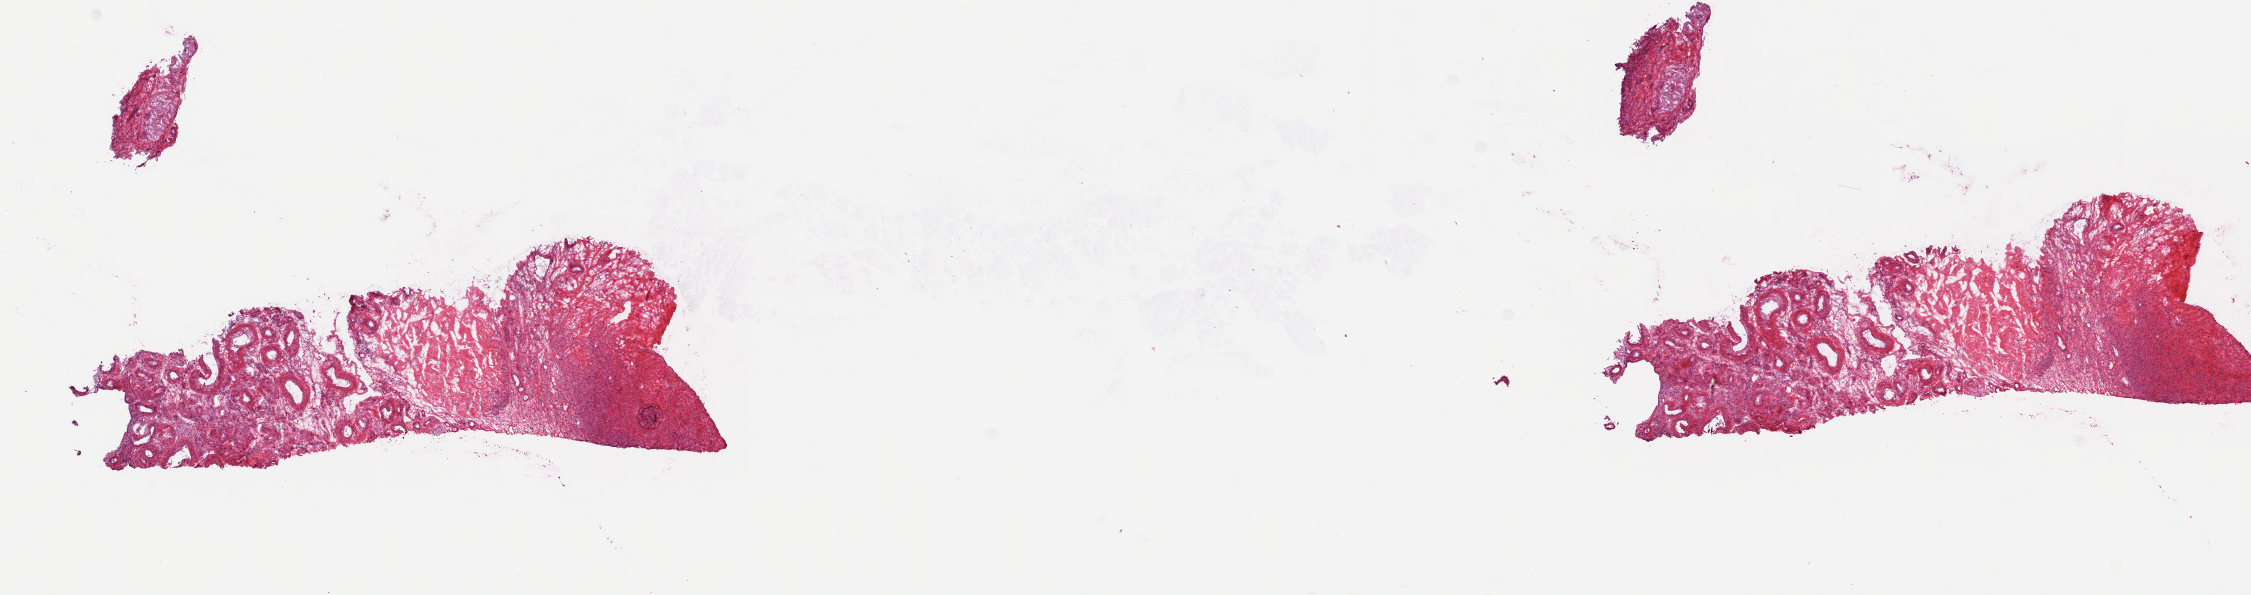
Whole-slide histology image, Hematoxylin and eosin (H&E) stained, low-resolution overview of the scanned area, about 17.9 x 4.7 mm (acquisition: 20x scan). Frozen section from the top of the tissue portion. Uterus, solid tissue normal (non-tumour tissue) sample. Patient: female, age at initial diagnosis 56 years. Slide review estimates, as recorded: tumour cells 0%, tumour nuclei 0%, normal cells 100%, stromal cells 0%, necrosis 0%. Infiltration values recorded for this section: lymphocyte infiltration 50%, monocyte infiltration 10%, neutrophil infiltration 10%.
This section: solid tissue normal sample (biorepository sample class). Patient diagnosis: Endometrioid adenocarcinoma, NOS (endometrium).